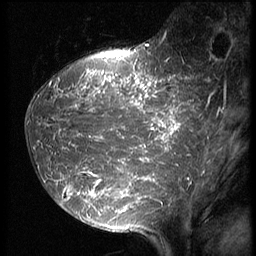
Breast MRI (dynamic contrast-enhanced), one sagittal slice; position 20 of 64 along the scan axis; 3 images stored at this slice position (order not interpretable as contrast timing); 1.5 T; TE 4.2 ms, TR 9 ms; 2.5 mm slice thickness; 256 × 256 image matrix, field of view 180 × 180 mm. Female patient, age 39 years. From the clinical record (not read from this slice): setting: breast cancer imaged before/during neoadjuvant chemotherapy; receptor status: HER2-positive.
Structures marked on this image (semi-automatically segmented with operator editing):
- analysis volume of interest (the breast-tissue region the enhancement analysis was run in; not a lesion): bounding box <25,47,210,239> (left, top, right, bottom; pixels)
- tumour enhancement mask (voxels above the 140 % enhancement threshold inside the analysis volume of interest): <39,51,210,218>